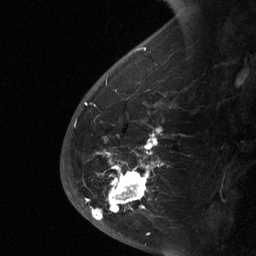
Breast MRI (dynamic contrast-enhanced), one sagittal slice; position 18 of 64 along the scan axis; dynamic contrast-enhanced study with each time point stored as its own series, time point 2 of 3 at this slice position (early post-contrast, ordered by acquisition time); 1.5 T; TE 4.8 ms, TR 27 ms; 256 × 256 image matrix, field of view 180 × 180 mm. Patient: female, 56 years. Case-level facts recorded for this patient, not image findings: setting: breast cancer imaged before/during neoadjuvant chemotherapy; receptor status: HER2-positive.
Annotated regions visible in this slice (semi-automatically segmented with operator editing):
- analysis volume of interest (the breast-tissue region the enhancement analysis was run in; not a lesion): bounding box <60,126,177,229> (left, top, right, bottom; pixels)
- tumour enhancement mask (voxels above the 90 % enhancement threshold inside the analysis volume of interest): <85,129,161,220>